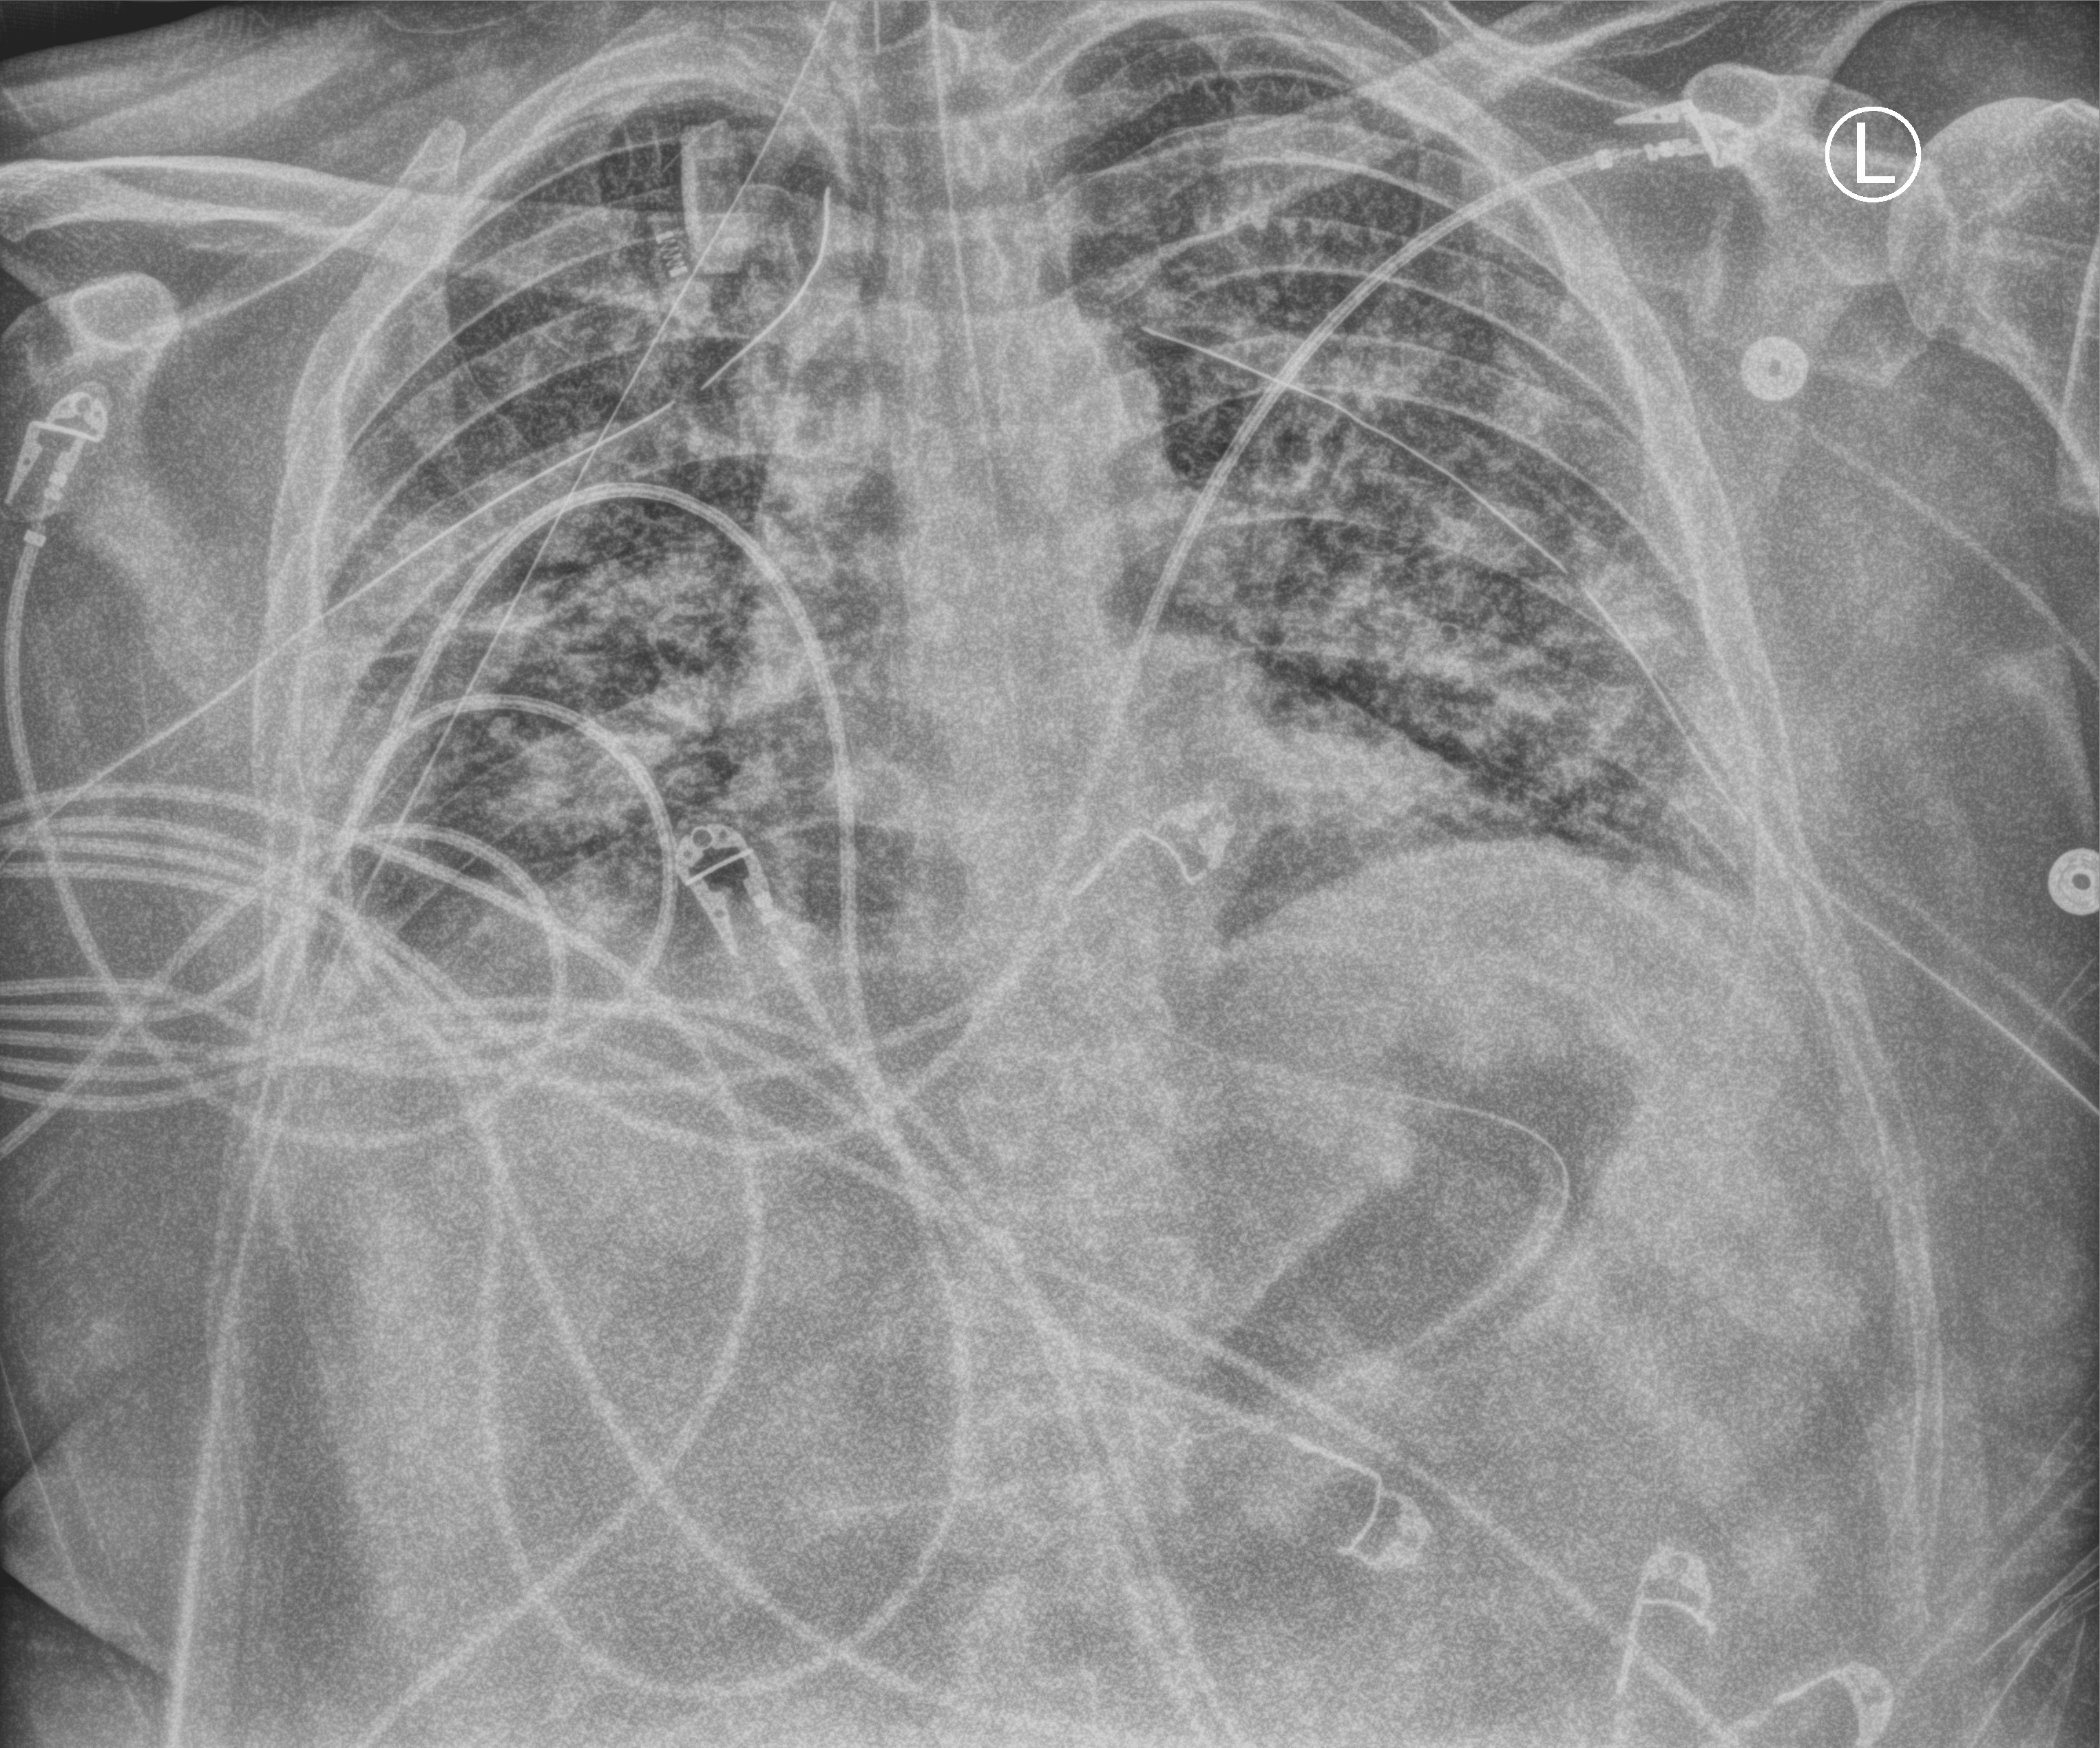
Portable chest radiograph; anteroposterior (AP) projection. Male patient hospitalised with COVID-19, age 18–59 years.
Hospital-stay facts (about this admission, not read from this image; timing relative to this image not recorded):
- diabetes (admission record): yes